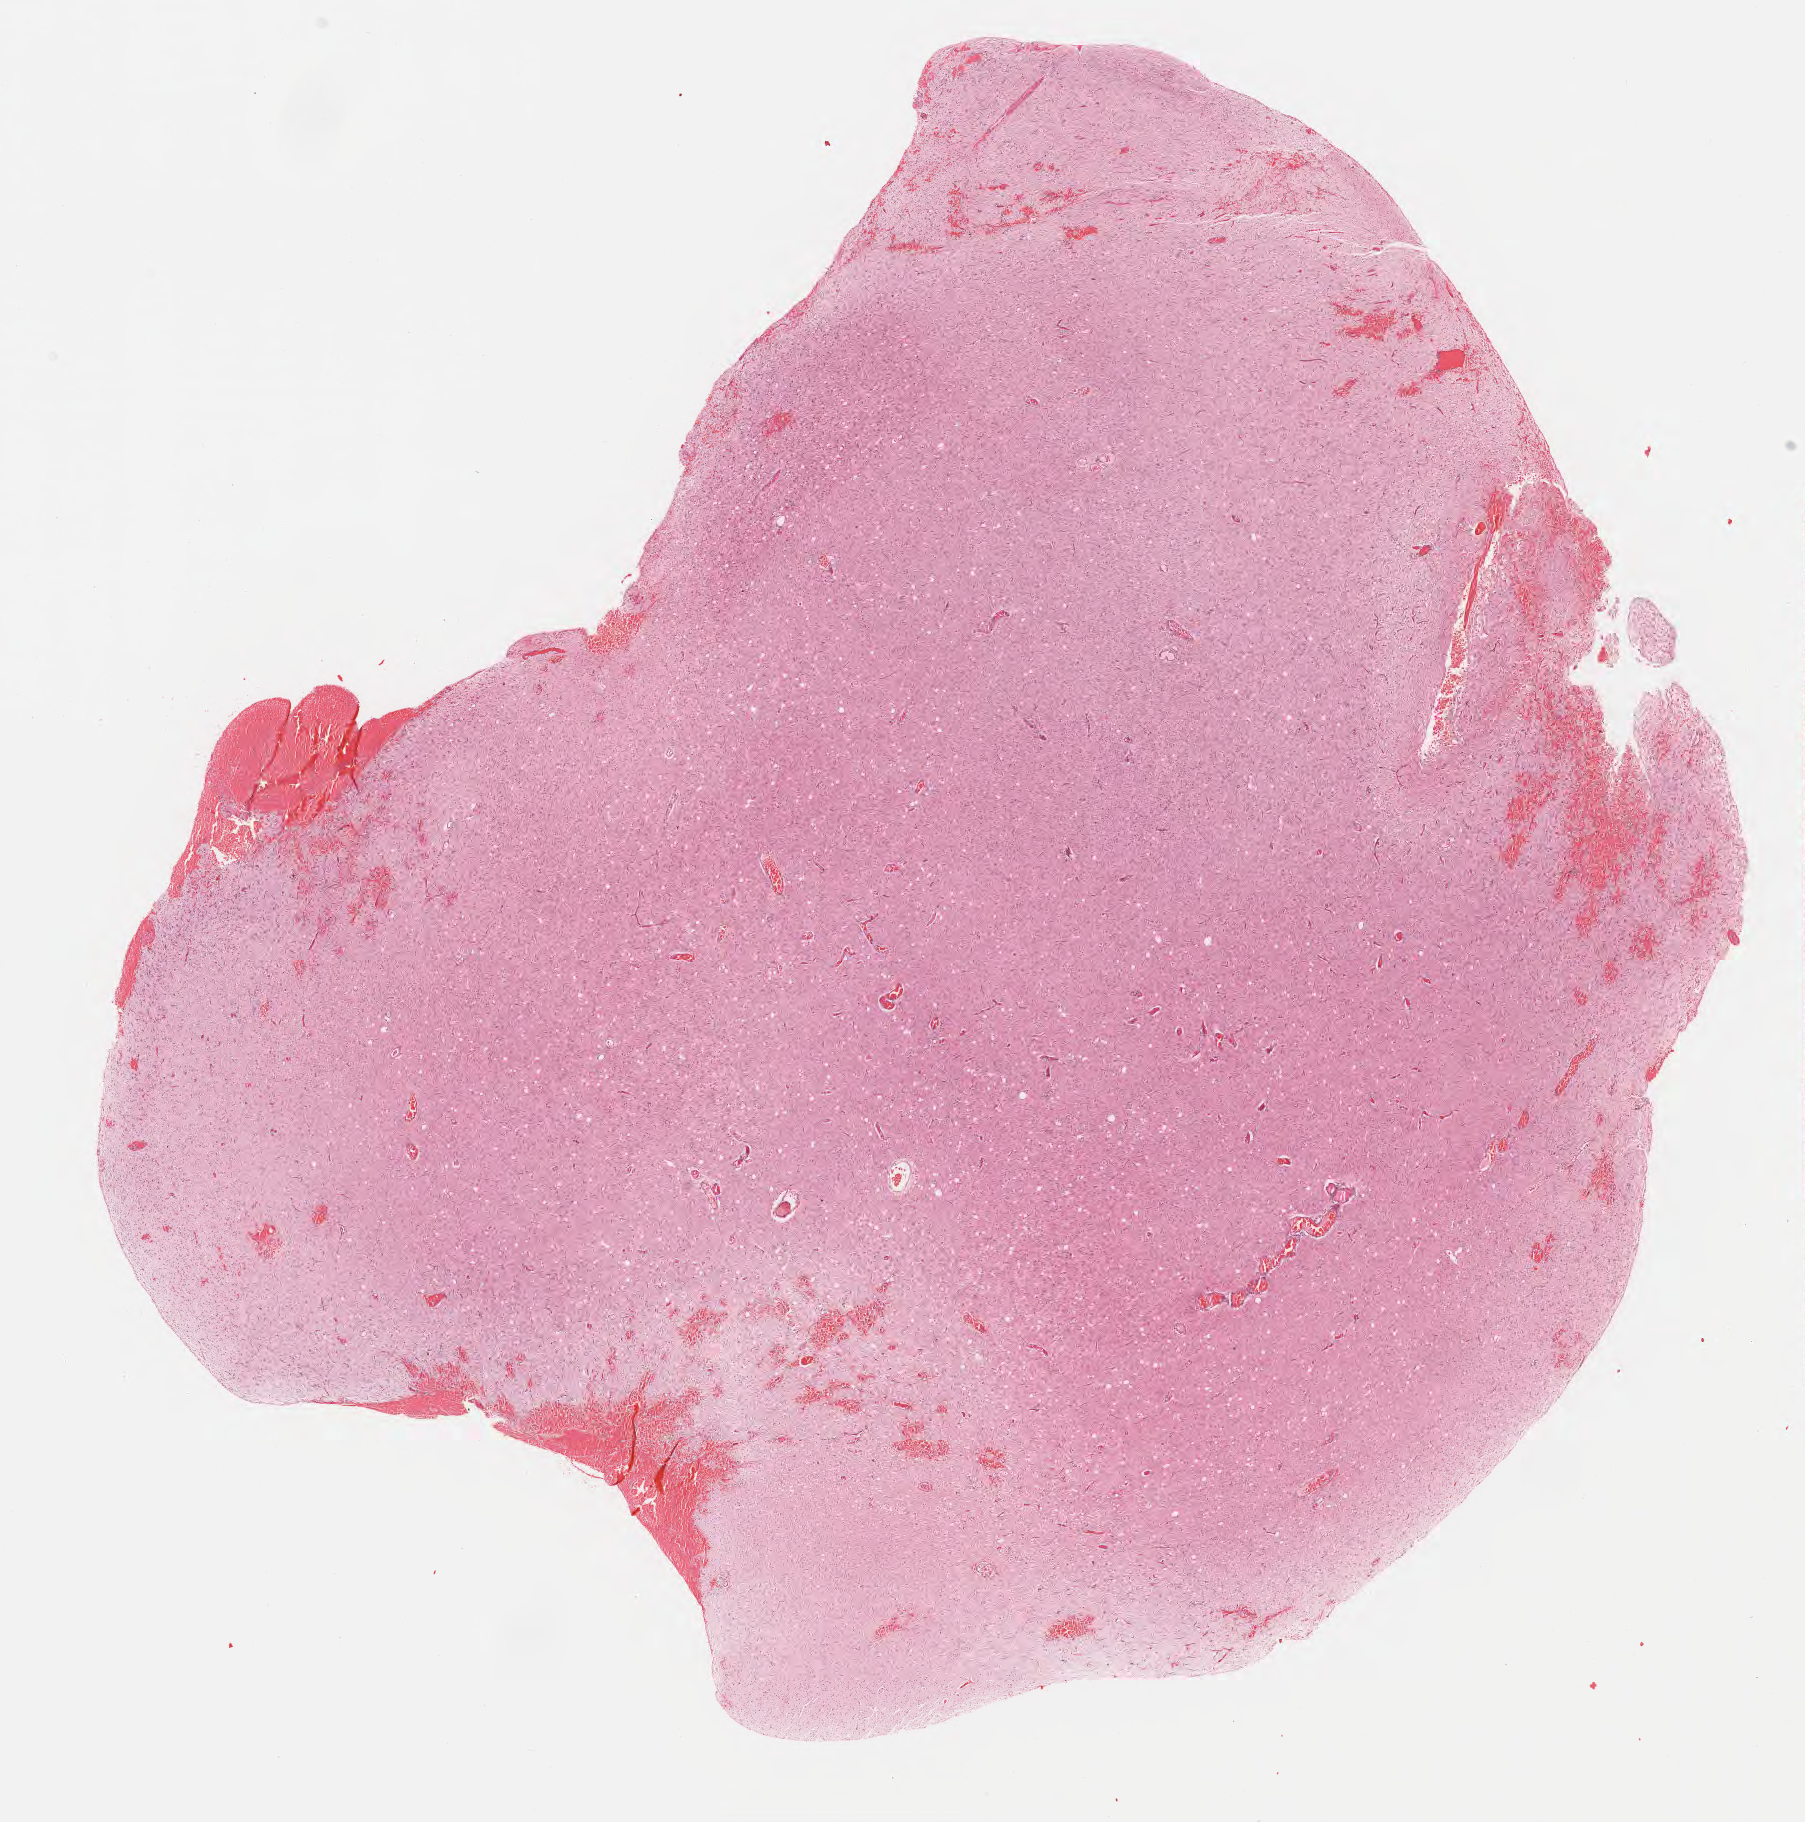
Whole-slide histology image, H&E — whole scanned area (about 14.6 x 14.7 mm) shown as a low-resolution overview; formalin-fixed paraffin-embedded (FFPE) diagnostic section; brain, primary tumour sample. Female patient; age at initial diagnosis 48 years. Histologic grade: G2 (moderately differentiated).
Diagnosis: Oligodendroglioma, NOS (cerebrum). Laterality: left.